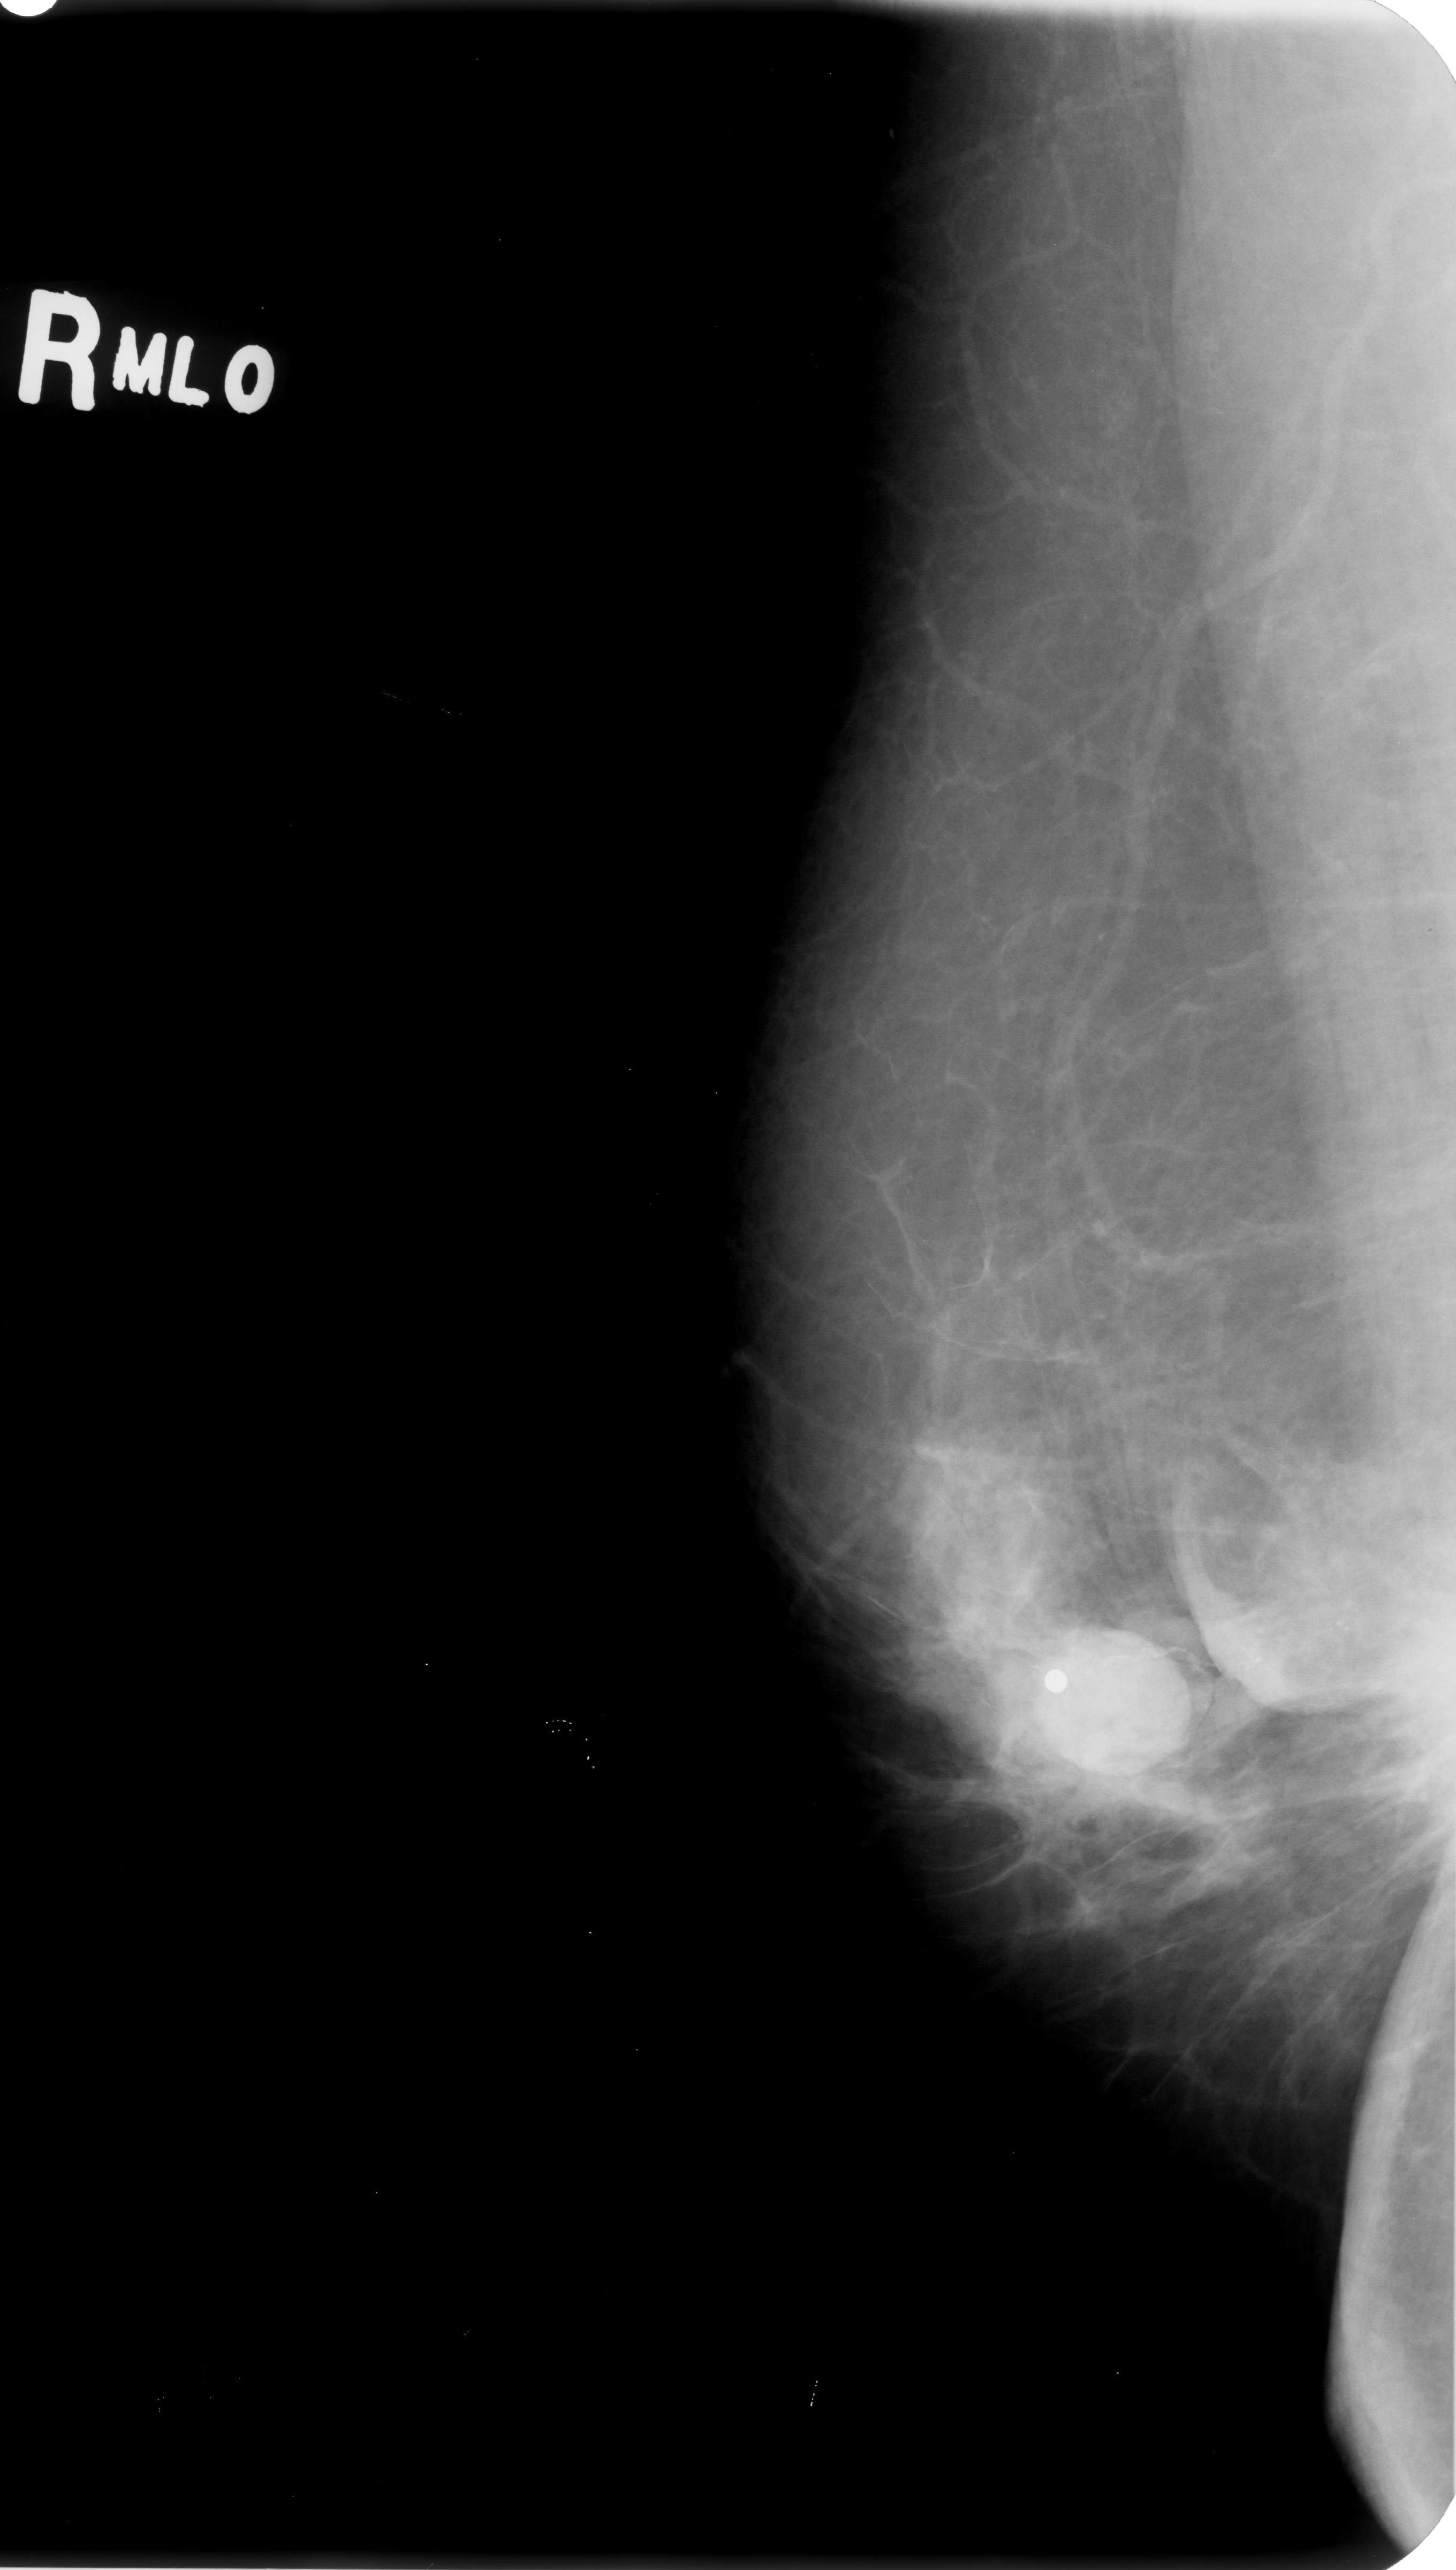
Mammogram (digitized film); right breast; mediolateral oblique (MLO) view; BI-RADS breast density category 2 (scale 1–4).
Marked findings (only marked abnormalities are described; nothing is implied about the rest of the image): mass, shape irregular, margins spiculated; BI-RADS assessment category 5; pathology (as recorded): malignant.